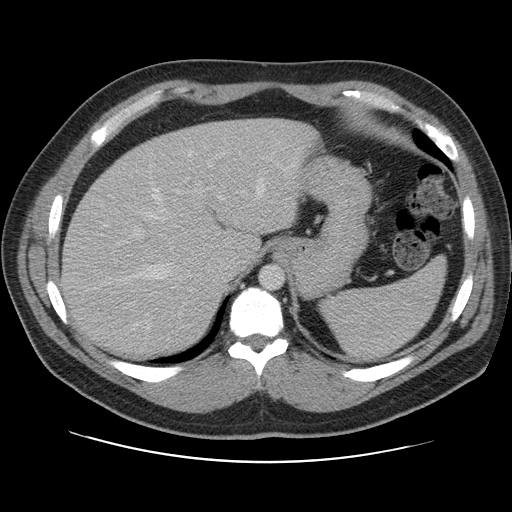
Contrast-enhanced abdominal CT, one axial slice. Position 83 of 109 along the scan axis. 120 kVp. Intravenous contrast given. Soft-tissue window (W 400 / L 40 HU). 5 mm slice thickness. 512 × 512 image matrix, field of view 402 × 402 mm. Male patient, age 35 years. Case-level facts recorded for this patient, not image findings: diagnosis: colorectal cancer liver metastases, imaged before liver resection; multiple liver metastases: yes; largest metastasis: 2.8 cm; chemotherapy before resection: yes.
Annotated regions visible in this slice (expert manual segmentation):
- hepatic veins: box from (x=118, y=177) to (x=266, y=323) px
- liver: (x=63, y=118)–(x=314, y=358)
- planned liver remnant (the part of the liver to remain after resection): (x=63, y=119)–(x=301, y=355)
- portal vein (with intrahepatic branches): (x=115, y=160)–(x=220, y=306)